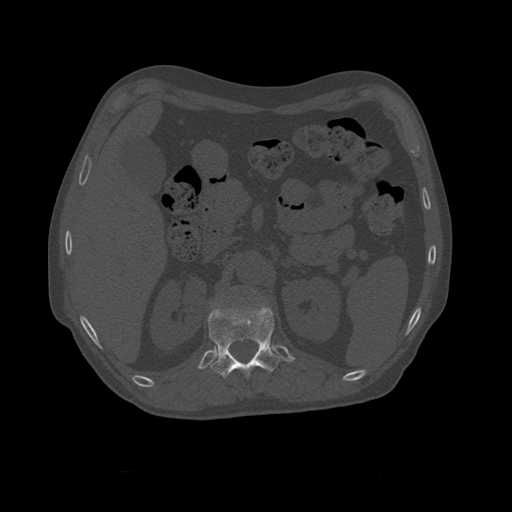
CT including the spine, one axial slice. Slice 377 of 450 in the series (ordered by position). 120 kVp. Bone window (W 1800 / L 400 HU). 512 × 512 image matrix, field of view 405 × 405 mm. Patient age 75 years. From the clinical record (not read from this slice): primary cancer: prostate.
Outlined on this slice (semi-automatically segmented with operator editing):
- L1 vertebra: box from (x=253, y=291) to (x=256, y=293) px
- T11 vertebra: (x=207, y=300)–(x=280, y=379)